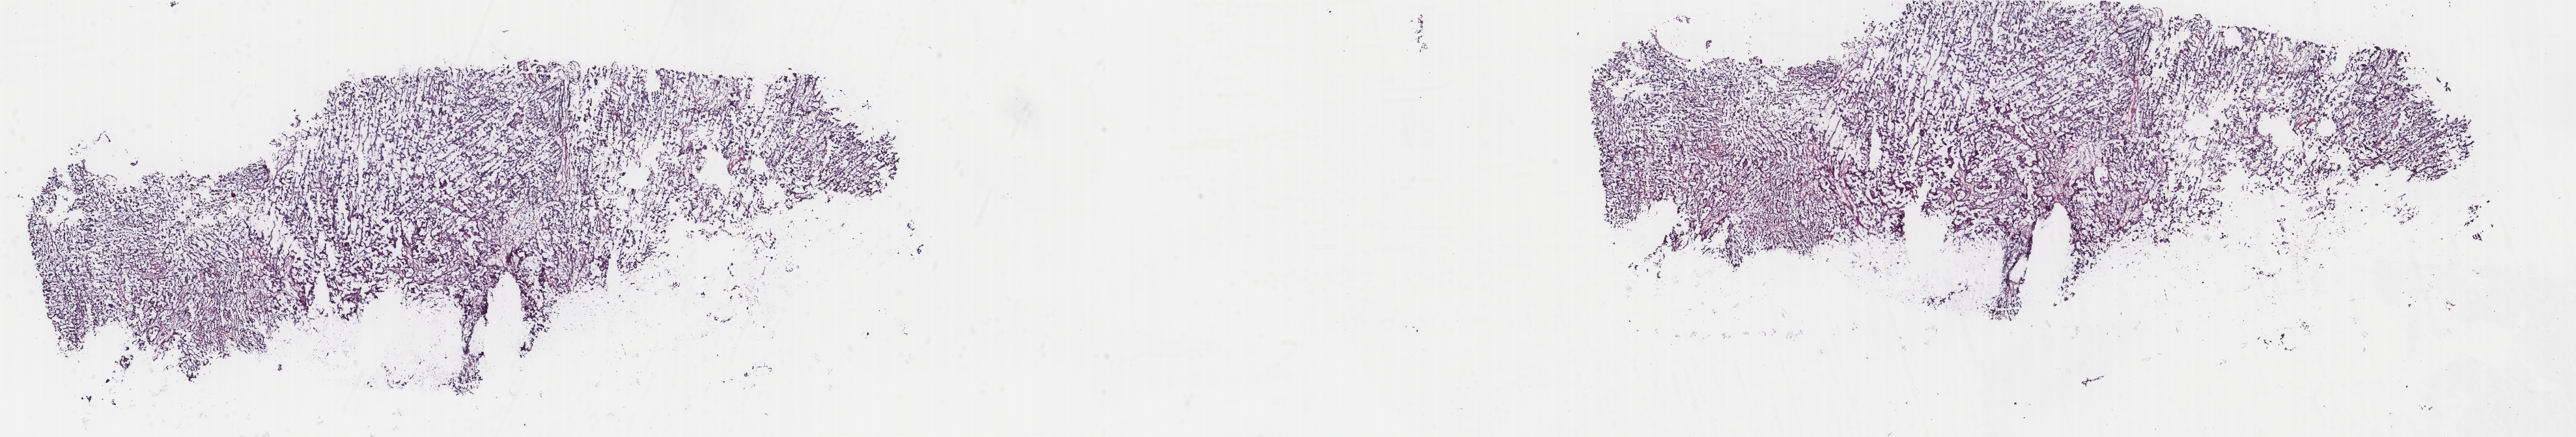
Digitized H&E-stained tissue section (whole slide) — whole scanned area (about 31.4 x 5.3 mm, acquisition: 40x scan) shown as a low-resolution overview. Frozen section. Primary tumour sample from the ovary. Female, age 60 years at initial diagnosis.
Histologic diagnosis: Serous cystadenocarcinoma, NOS (retroperitoneum).